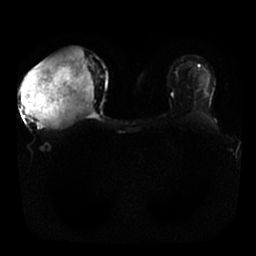
Breast MRI, one axial slice. Slice 14 of 25 in the series (ordered by position). Diffusion-weighted series; image 2 of 4 stored at this slice position (different b-values; order by instance number). 1.5 T. 4 mm slice thickness. 256 × 256 image matrix, field of view 340 × 340 mm. Female patient.
Annotated regions visible in this slice (expert manual segmentation):
- tumour on diffusion-weighted imaging: box from (x=21, y=47) to (x=95, y=130) px